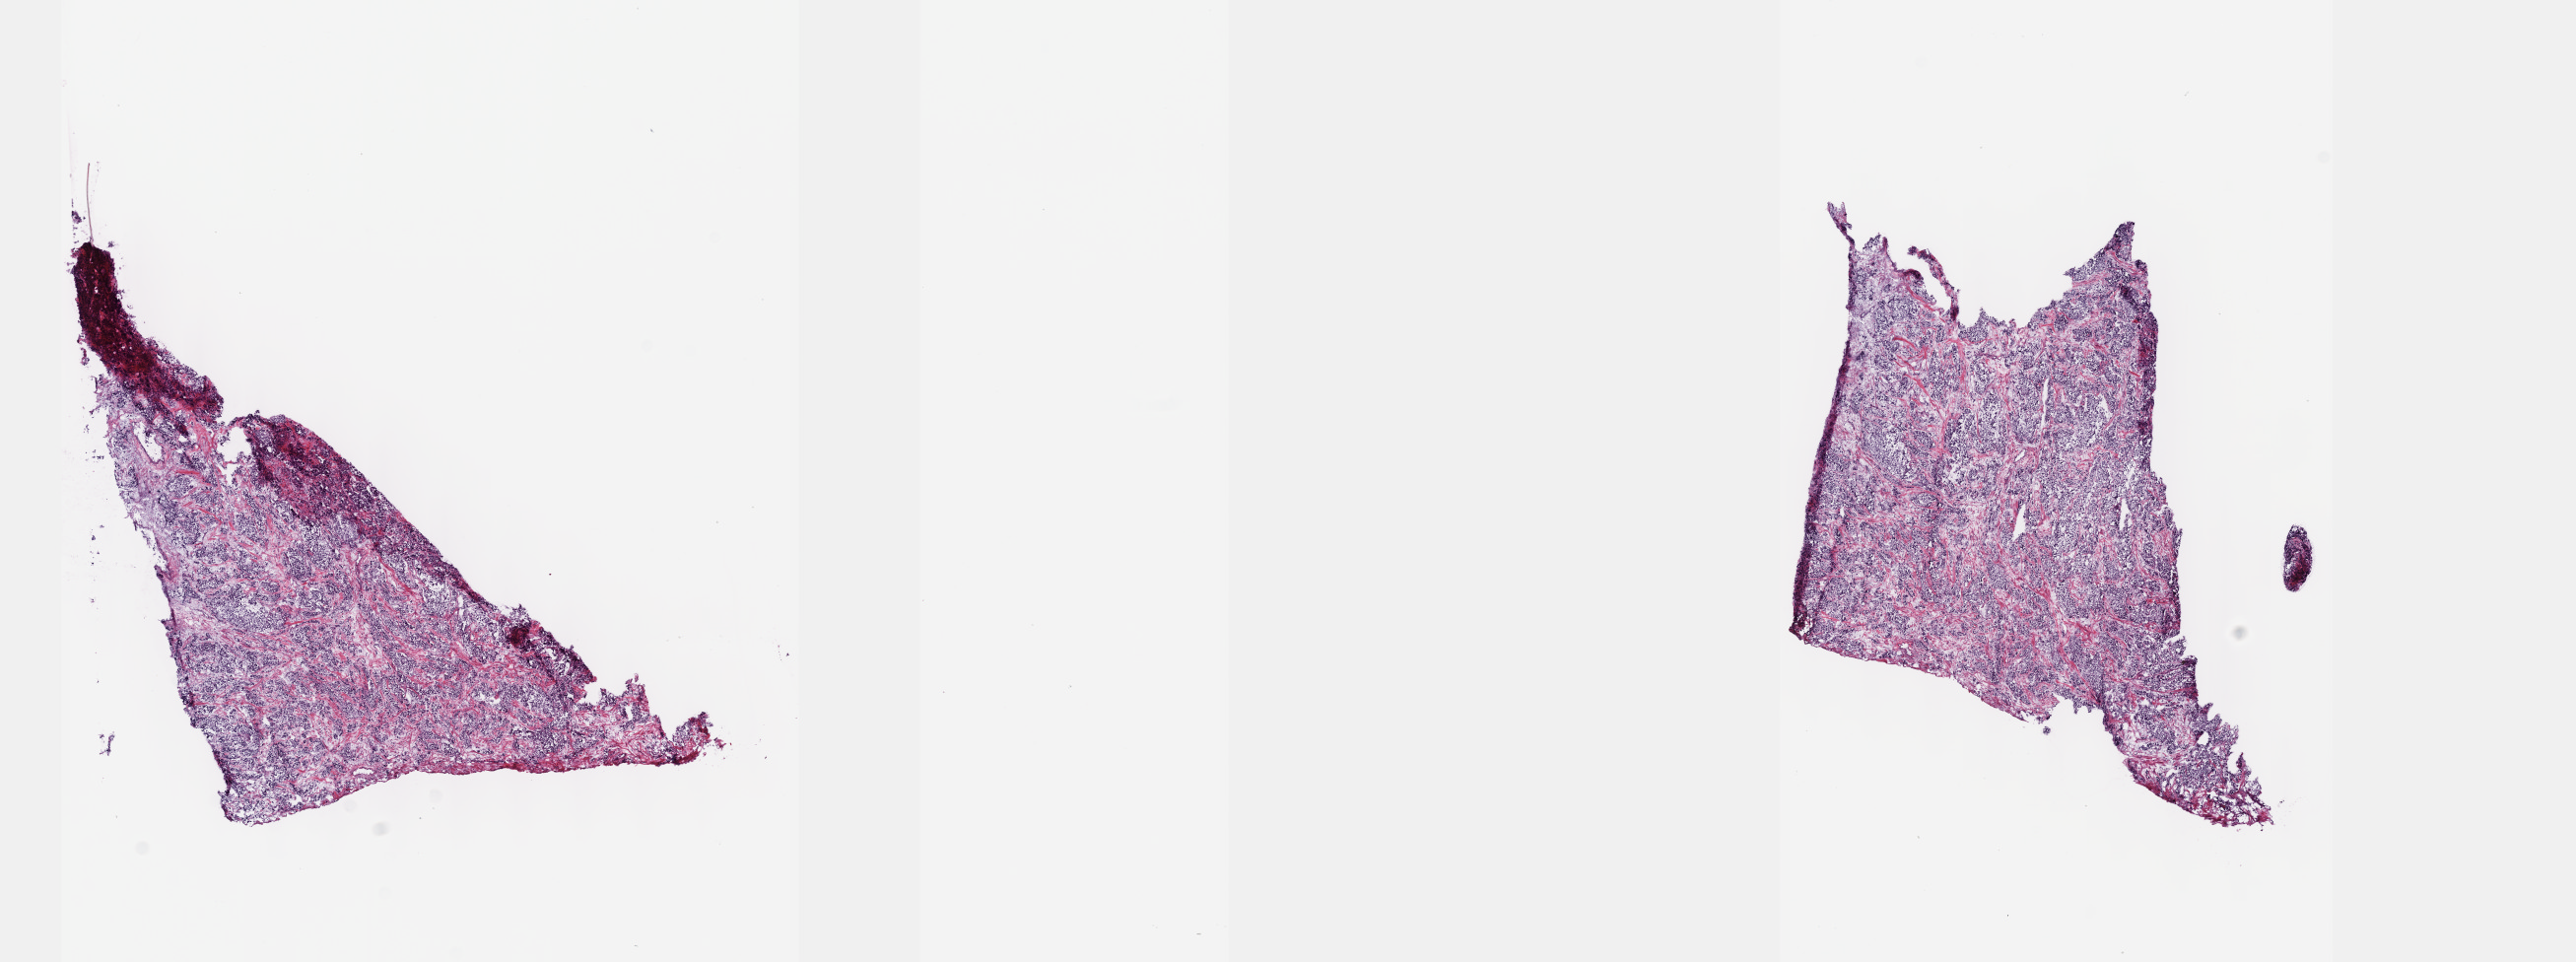
H&E whole-slide image — low-resolution overview of the scanned area, about 21.1 x 7.9 mm (slide scanned at 40x). Frozen section from the top of the tissue portion. Sample: primary tumour, adrenal gland. Male, age 34 years at initial diagnosis. Slide review estimates, as recorded: tumour cells 100%, tumour nuclei 75%, normal cells 0%, stromal cells 0%, necrosis 0%. Inflammatory infiltration, as recorded: lymphocyte infiltration 2%, monocyte infiltration 0%, neutrophil infiltration 0%.
Histologic diagnosis: Pheochromocytoma, NOS.